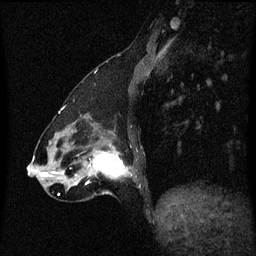
Breast MRI (dynamic contrast-enhanced), one sagittal slice; slice 18 of 60 in the series (ordered by position); dynamic contrast-enhanced series, image 2 of 3 at this slice position (ordered by acquisition); 1.5 T; TE 4.2 ms, TR 8.4 ms; 2 mm slice thickness; 256 × 256 image matrix. Female patient, age 47 years.
Outlined on this slice (semi-automatic segmentation, software-assisted and operator-edited):
- analysis volume of interest (the breast-tissue region the enhancement analysis was run in; not a lesion): bounding box <81,140,134,195> (left, top, right, bottom; pixels)
- tumour enhancement mask (voxels above the 70 % enhancement threshold inside the analysis volume of interest): <86,152,128,185>